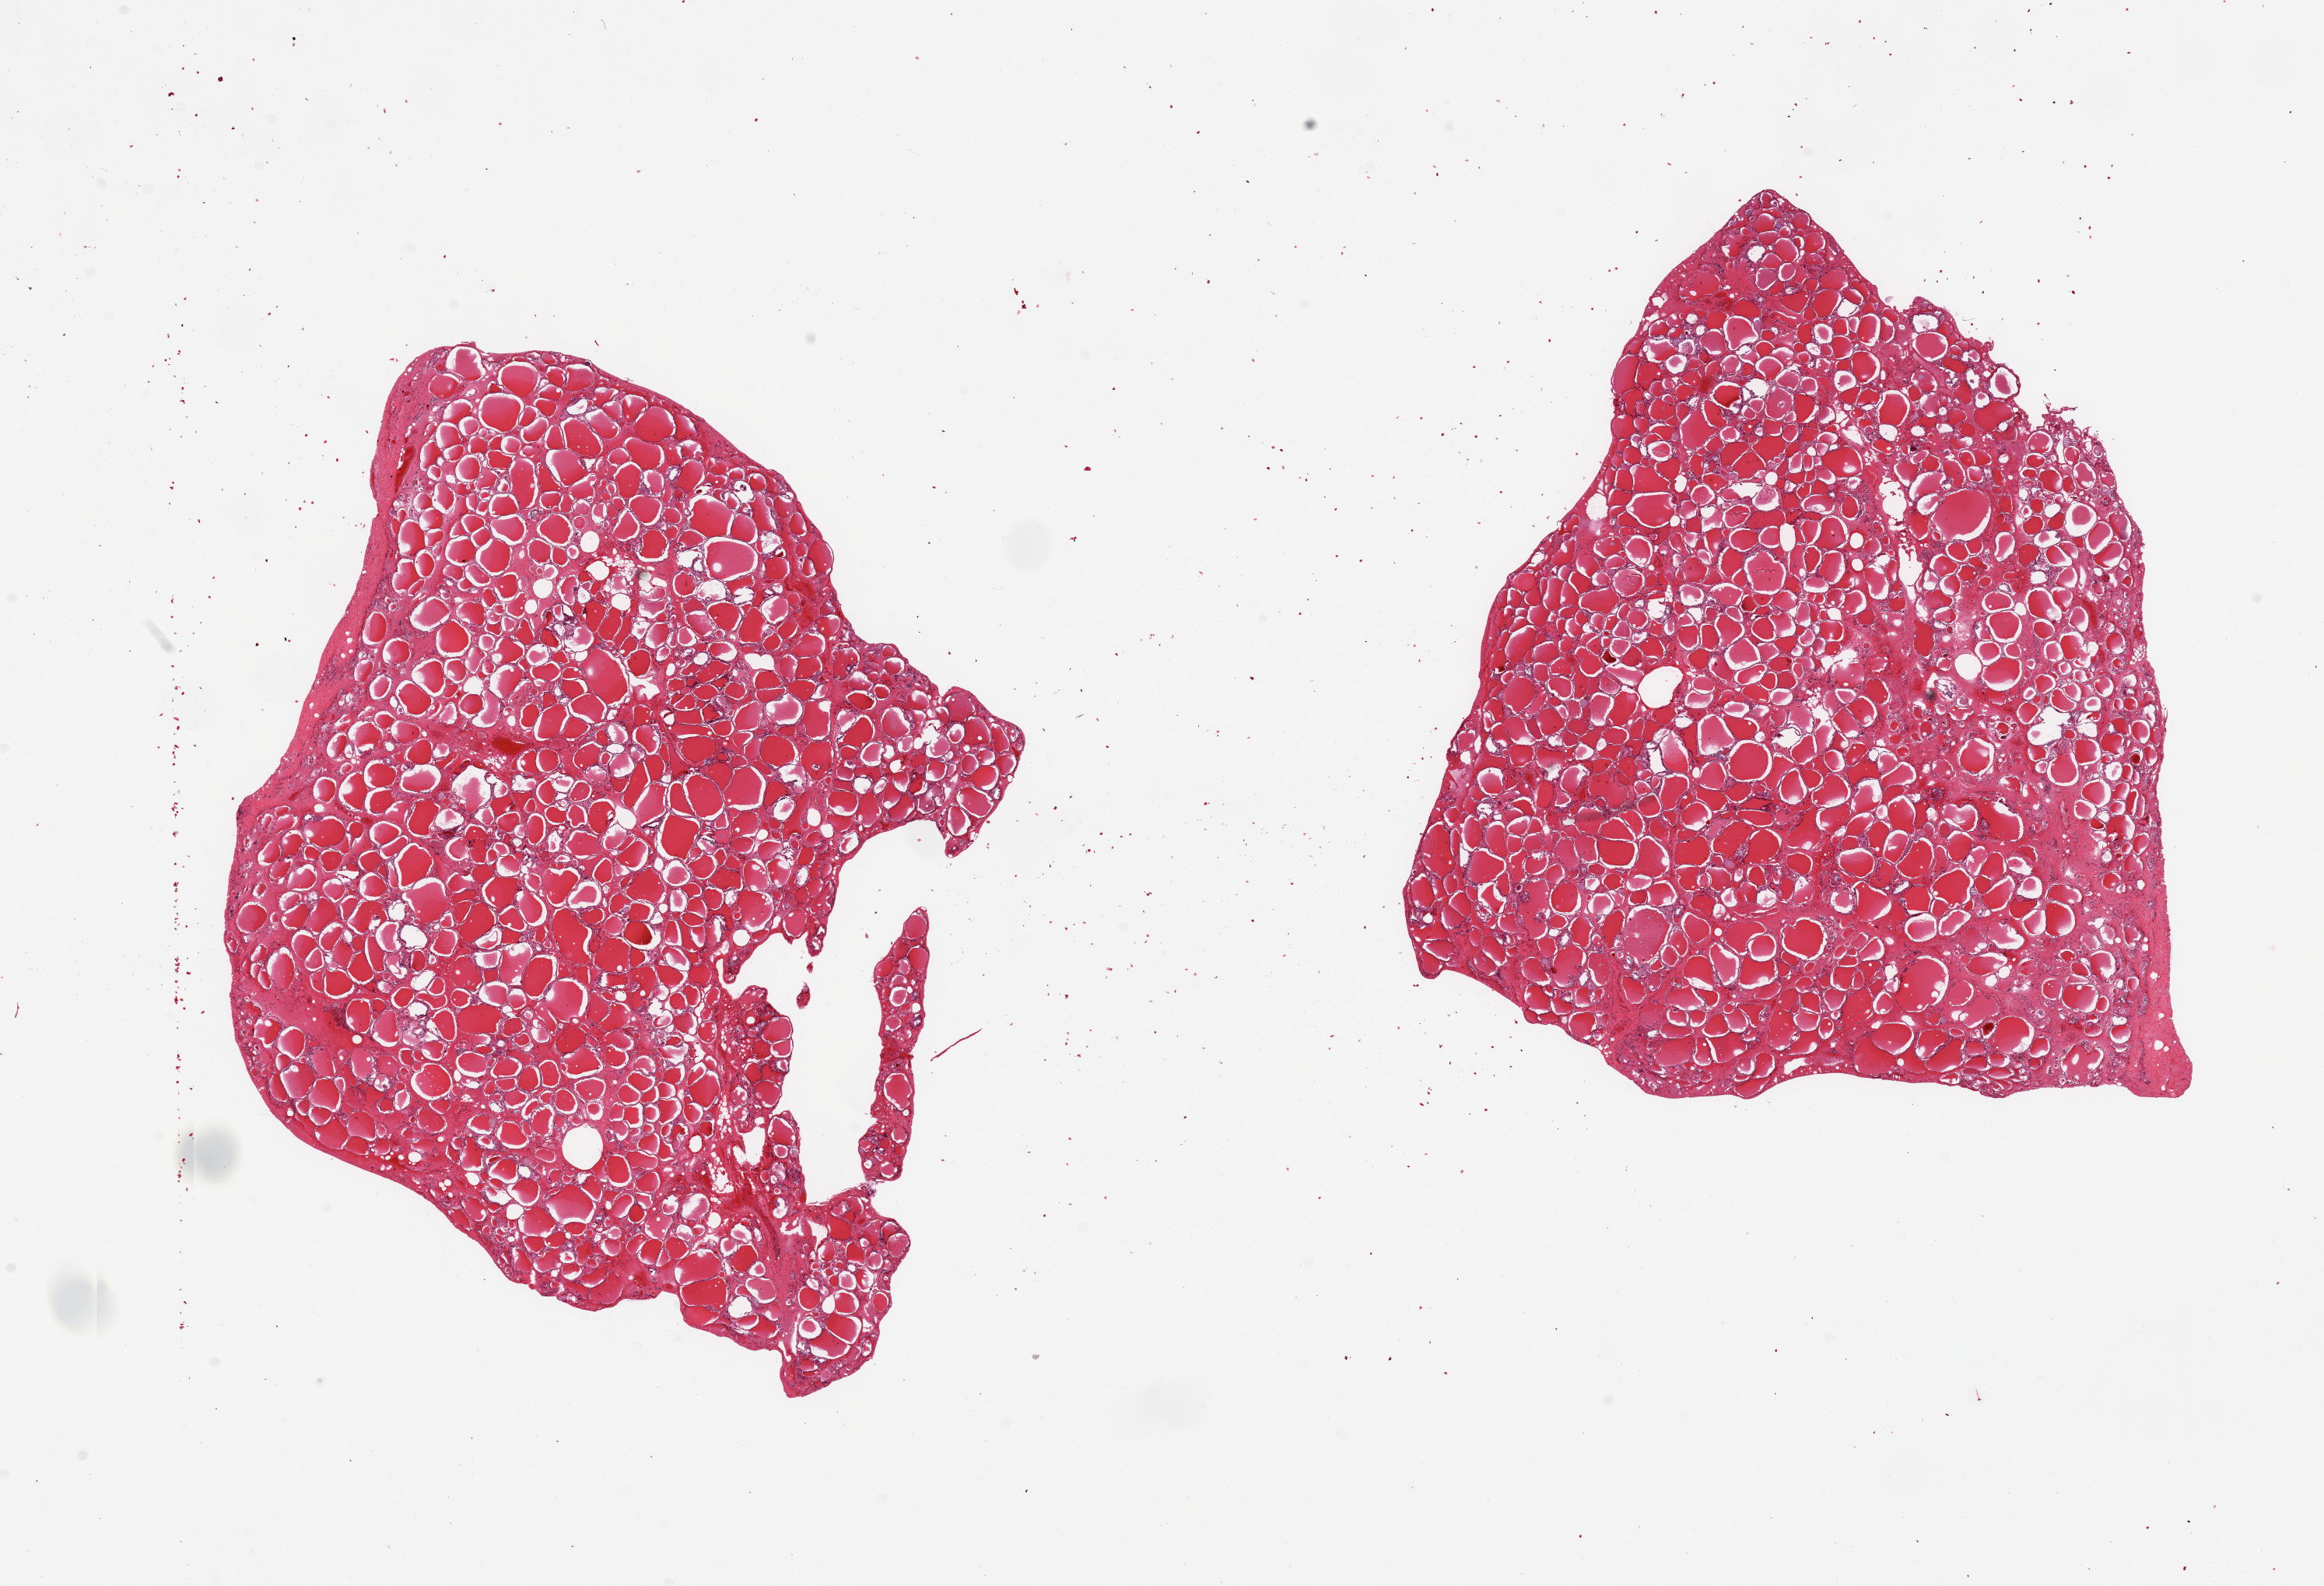
Digitized haematoxylin and eosin-stained section — whole scanned area (about 23.6 x 16.1 mm, acquisition: 20x scan) shown as a low-resolution overview, PAXgene-fixed, paraffin-embedded tissue, sampled site (target tissue): thyroid, donor tissue sample.
Review note (as recorded): 2 pieces.